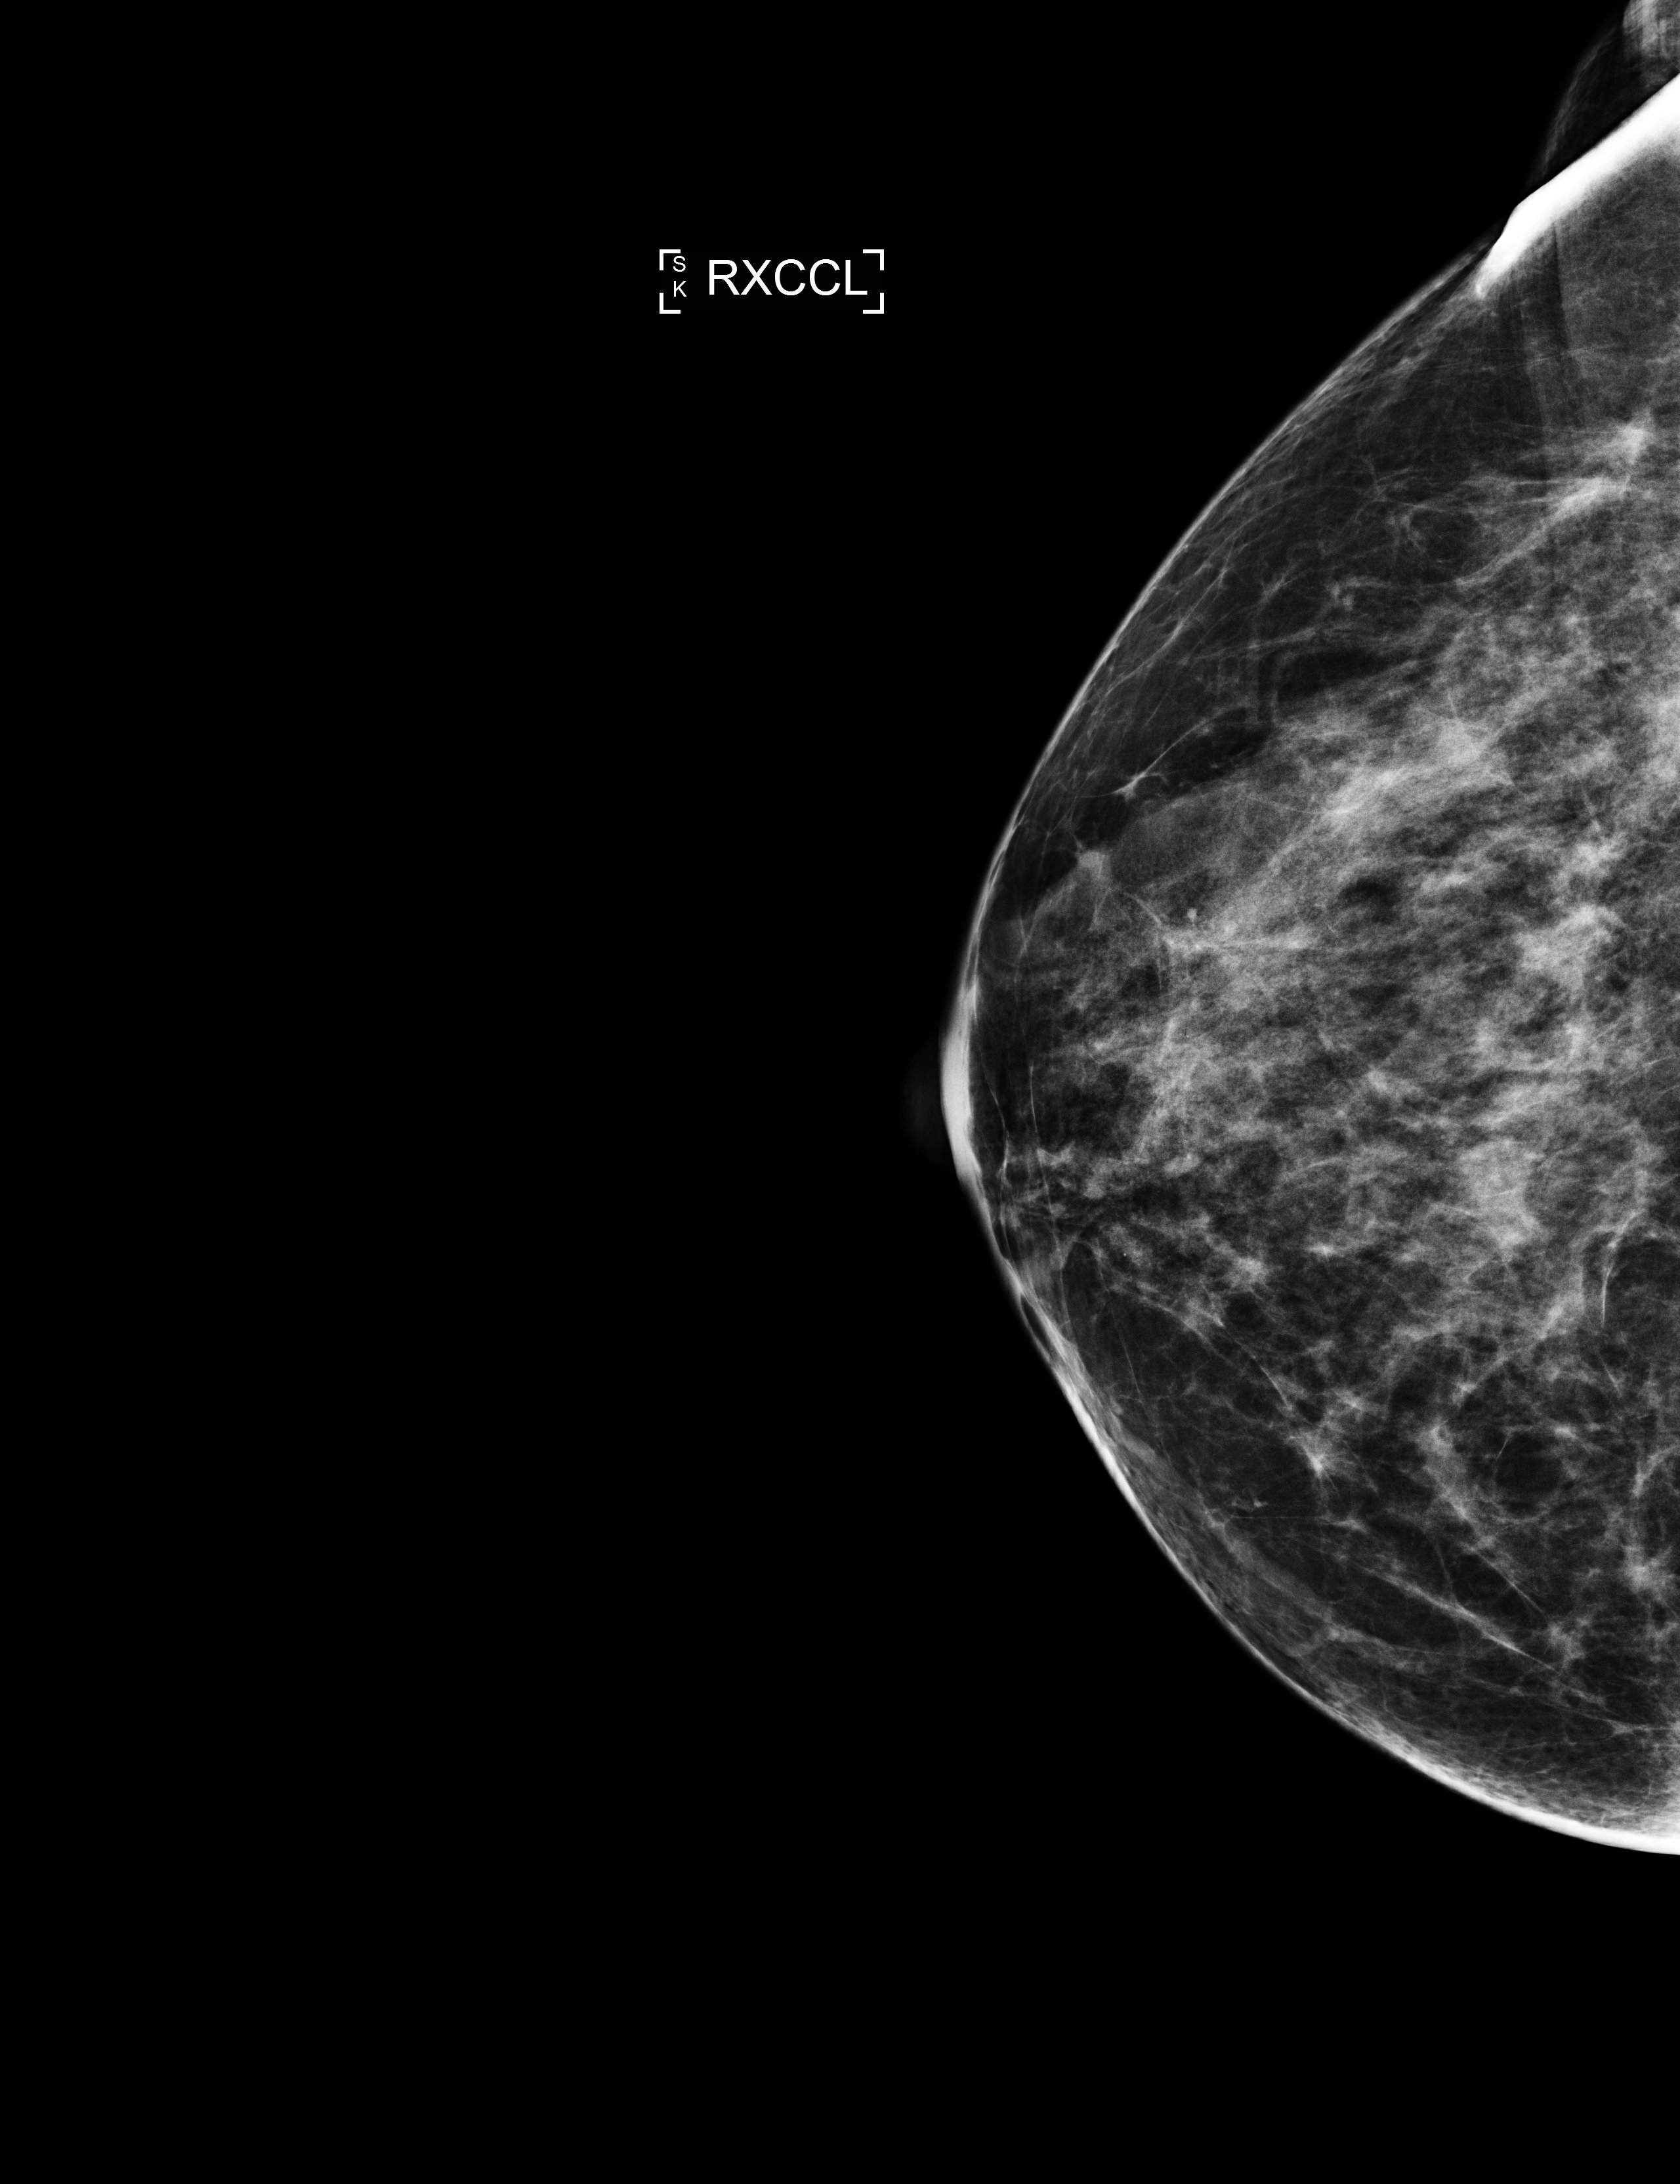
Full-field digital mammogram (FFDM); right breast; exaggerated CC view (lateral); annual screening mammography examination; compressed breast thickness 56 mm. Patient aged 59 years (female).
- breast density at the screening exam (both breasts): heterogeneously dense (BI-RADS density category c)
- final BI-RADS category for the screening round (tomosynthesis exam, both breasts): category 1
- recall: no recall after this screen